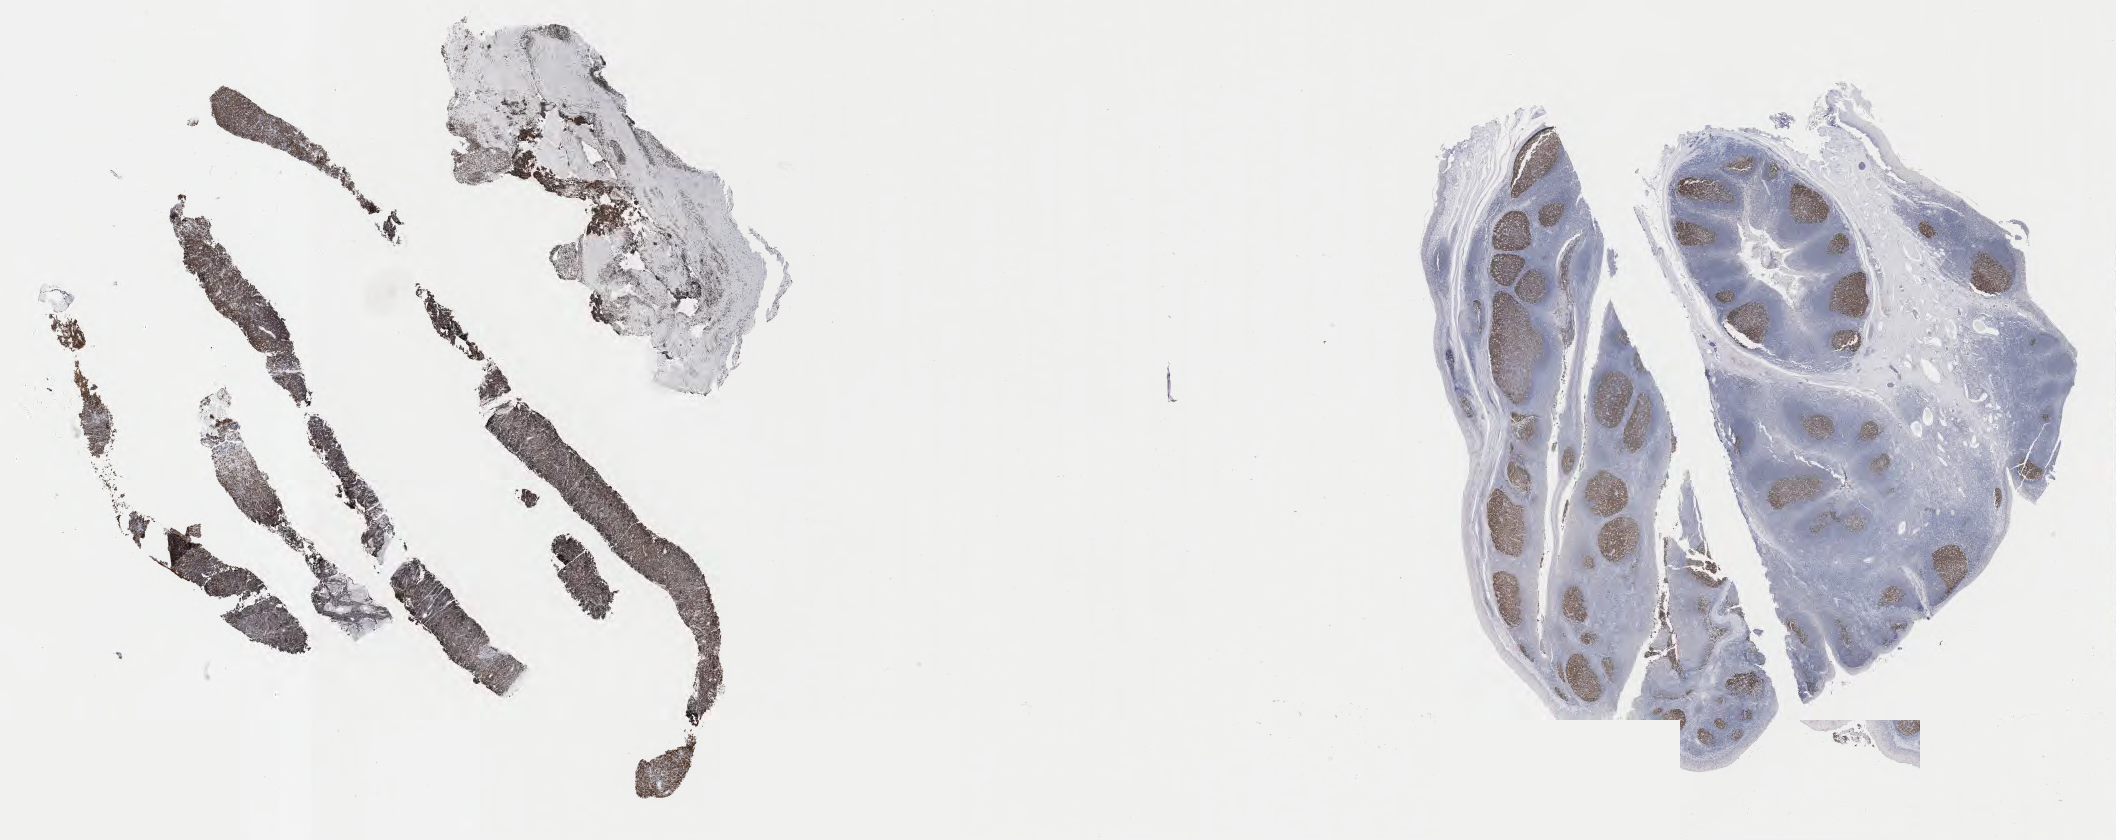
Whole-slide image, immunohistochemical stain for BCL6 — low-resolution overview of the scanned area, about 34.2 x 13.6 mm. Specimen: tumor tissue. Male patient, 29 years old.
Histologic diagnosis: Burkitt lymphoma, NOS.